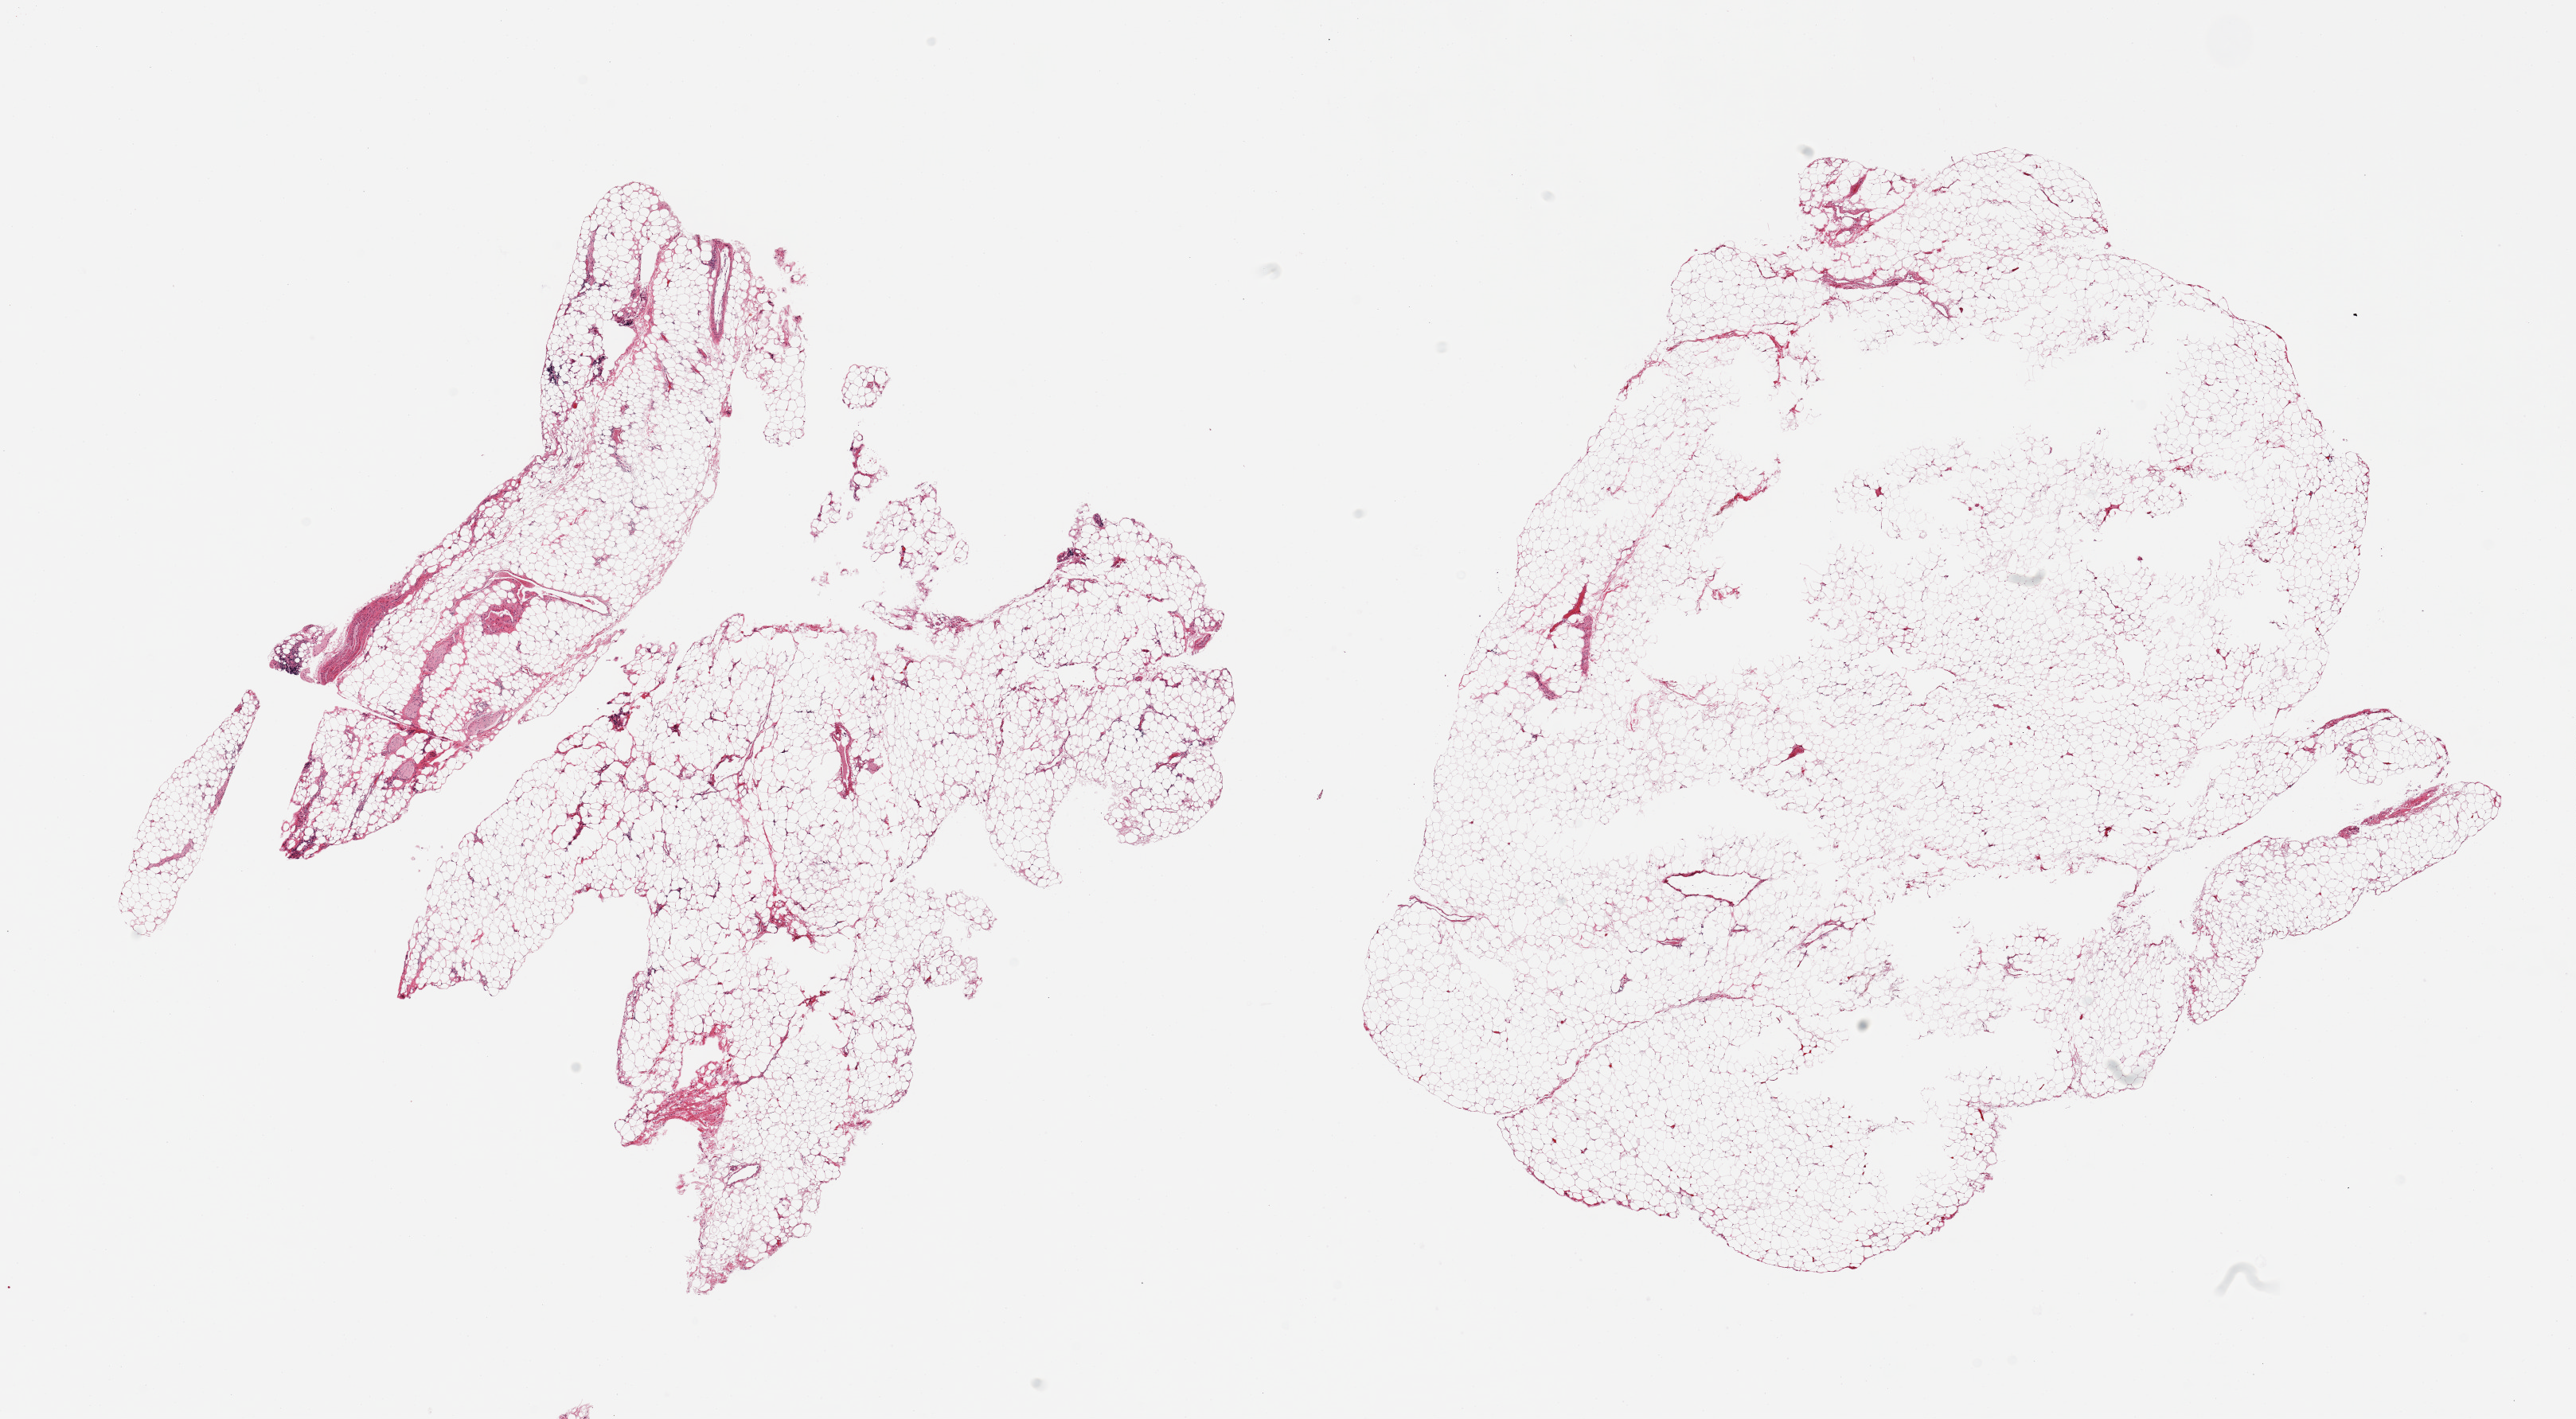
Hematoxylin and eosin (H&E) whole-slide image, brightfield — whole scanned area (about 25.6 x 14.1 mm, slide scanned at 20x) shown as a low-resolution overview, PAXgene-fixed paraffin-embedded (PFPE) section, sampled site (target tissue): prostate, donor tissue sample. Donor: male.
Pathologist's review note for this sample: 2 pieces; fat only.